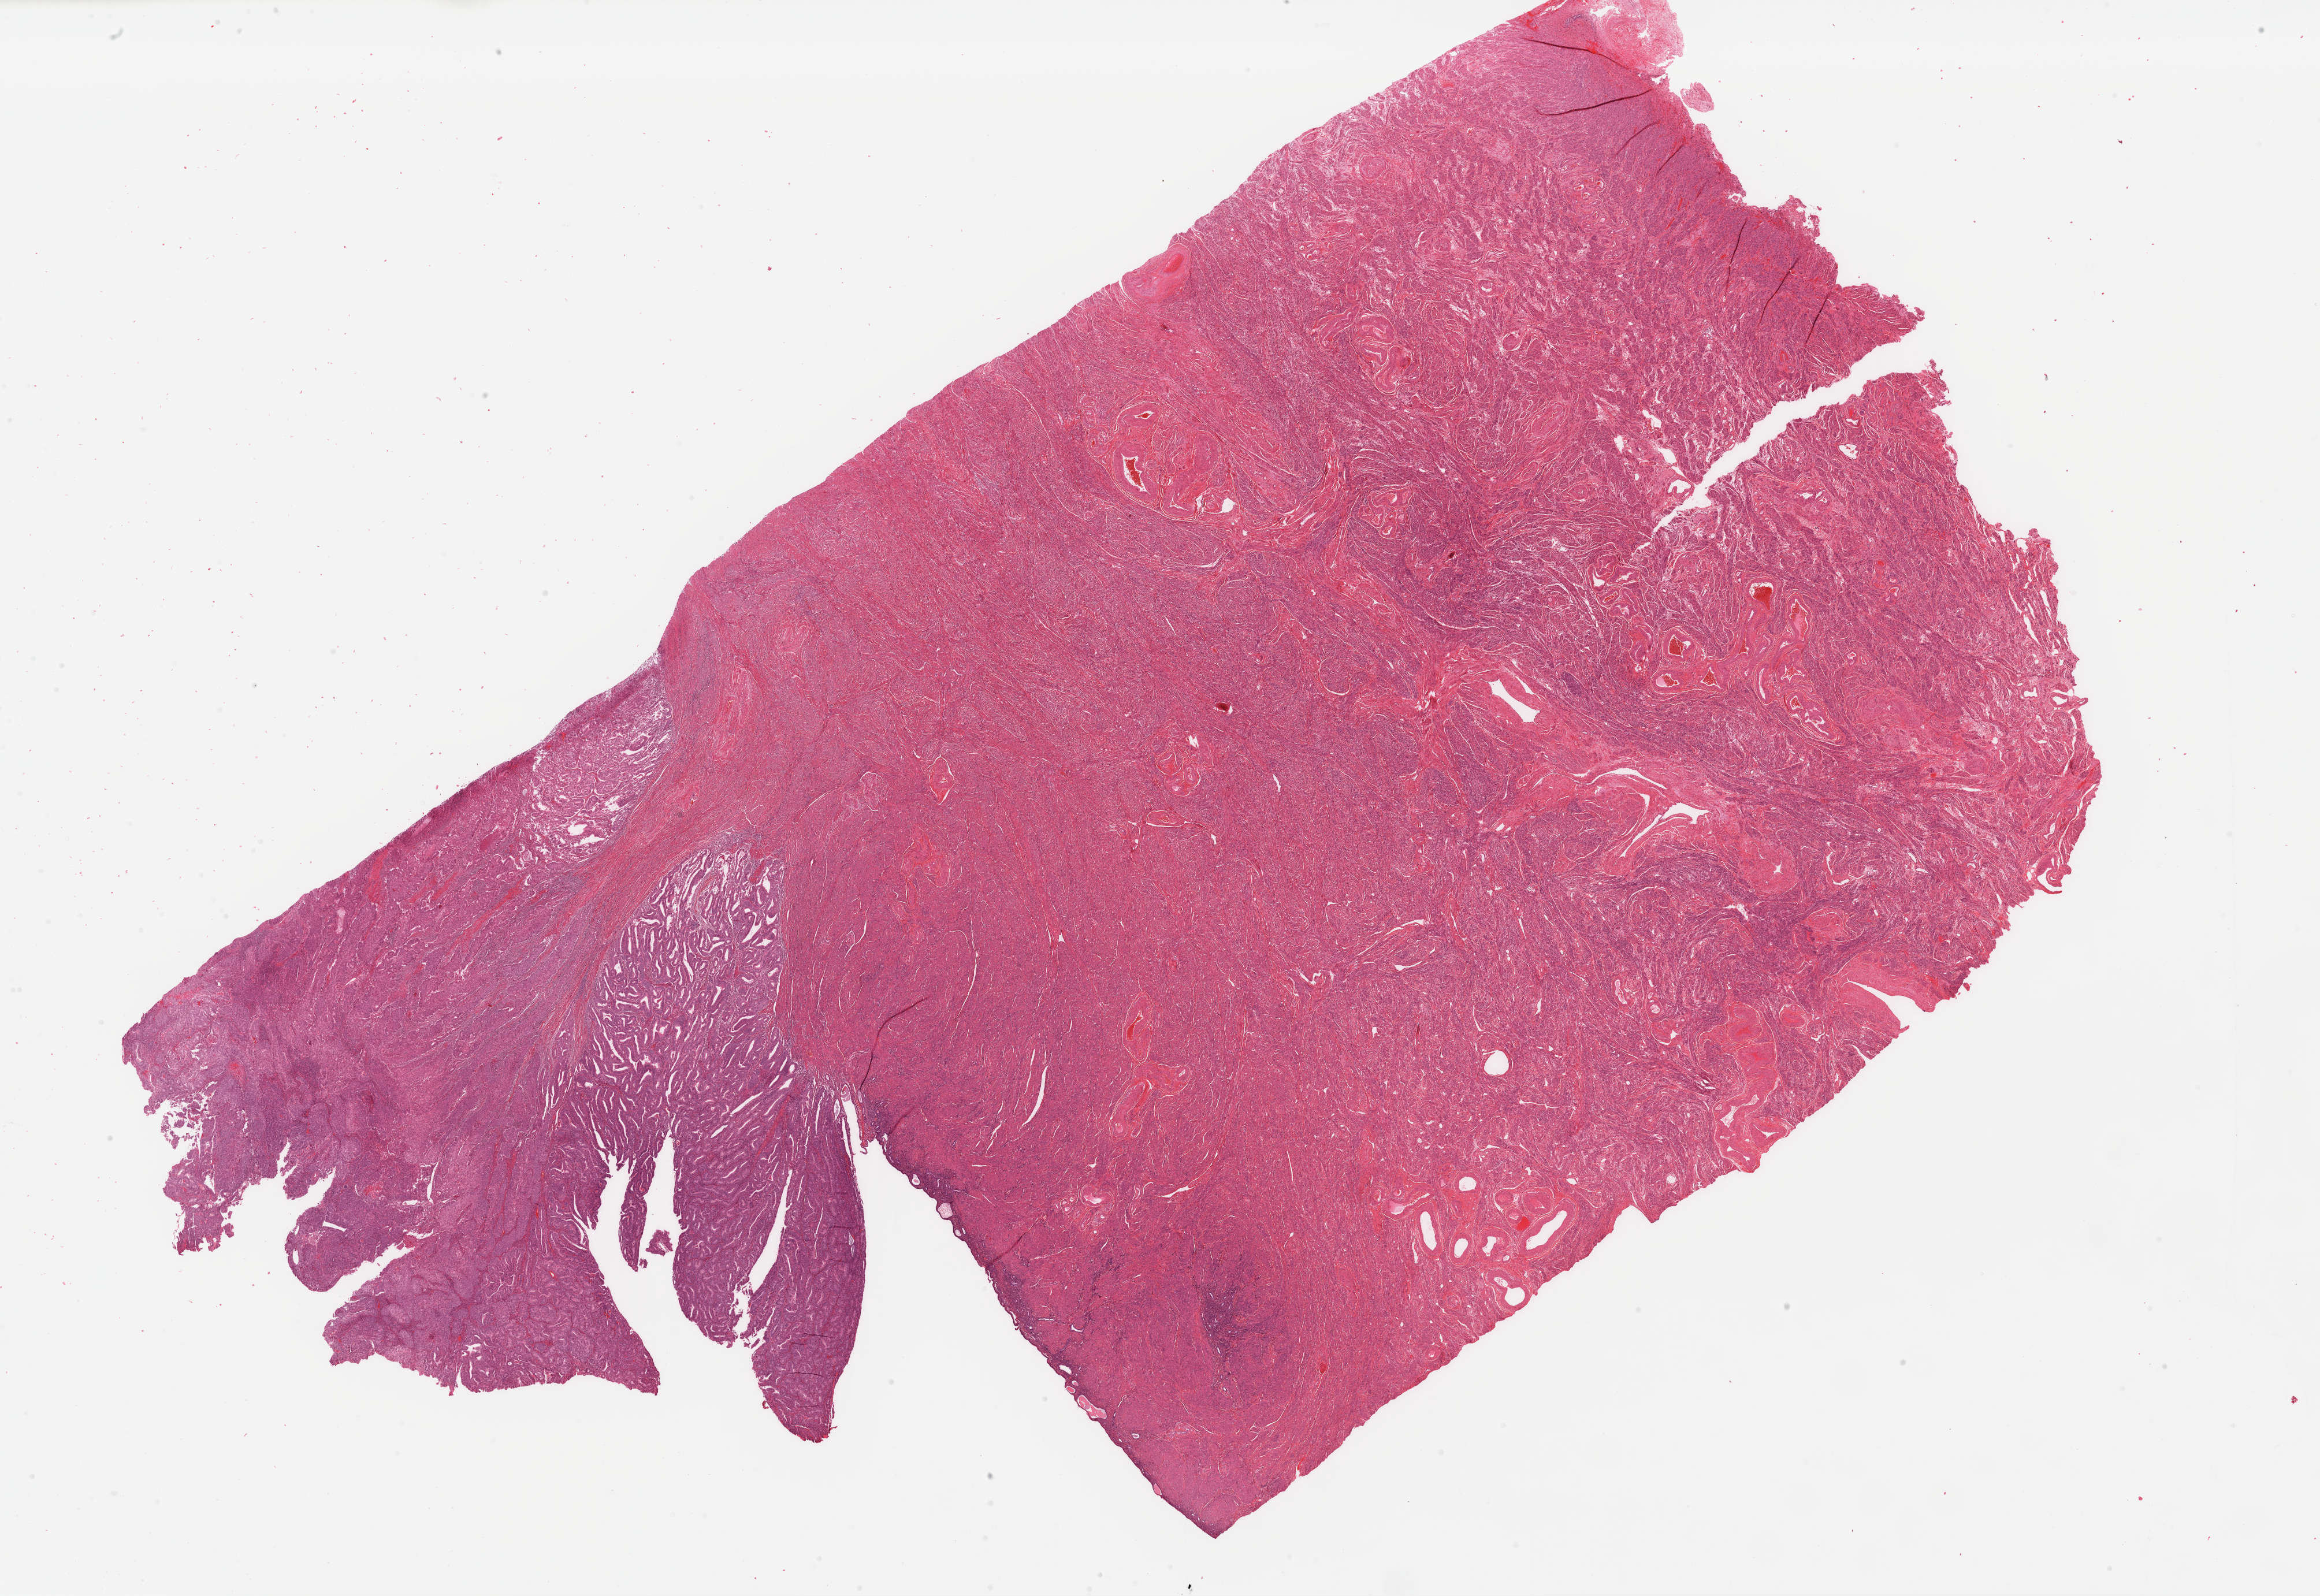
Whole-slide histology image, H&E-stained, low-resolution overview of the scanned area, about 31.7 x 21.8 mm. Formalin-fixed paraffin-embedded (FFPE) diagnostic section. Sample: primary tumour, uterus. Female, age 63 years at initial diagnosis. Histologic grade: G2 (moderately differentiated).
Pathologic diagnosis: Endometrioid adenocarcinoma, NOS (endometrium). FIGO stage: IB. Lymph nodes positive (case pathology): 0 of 3 examined.